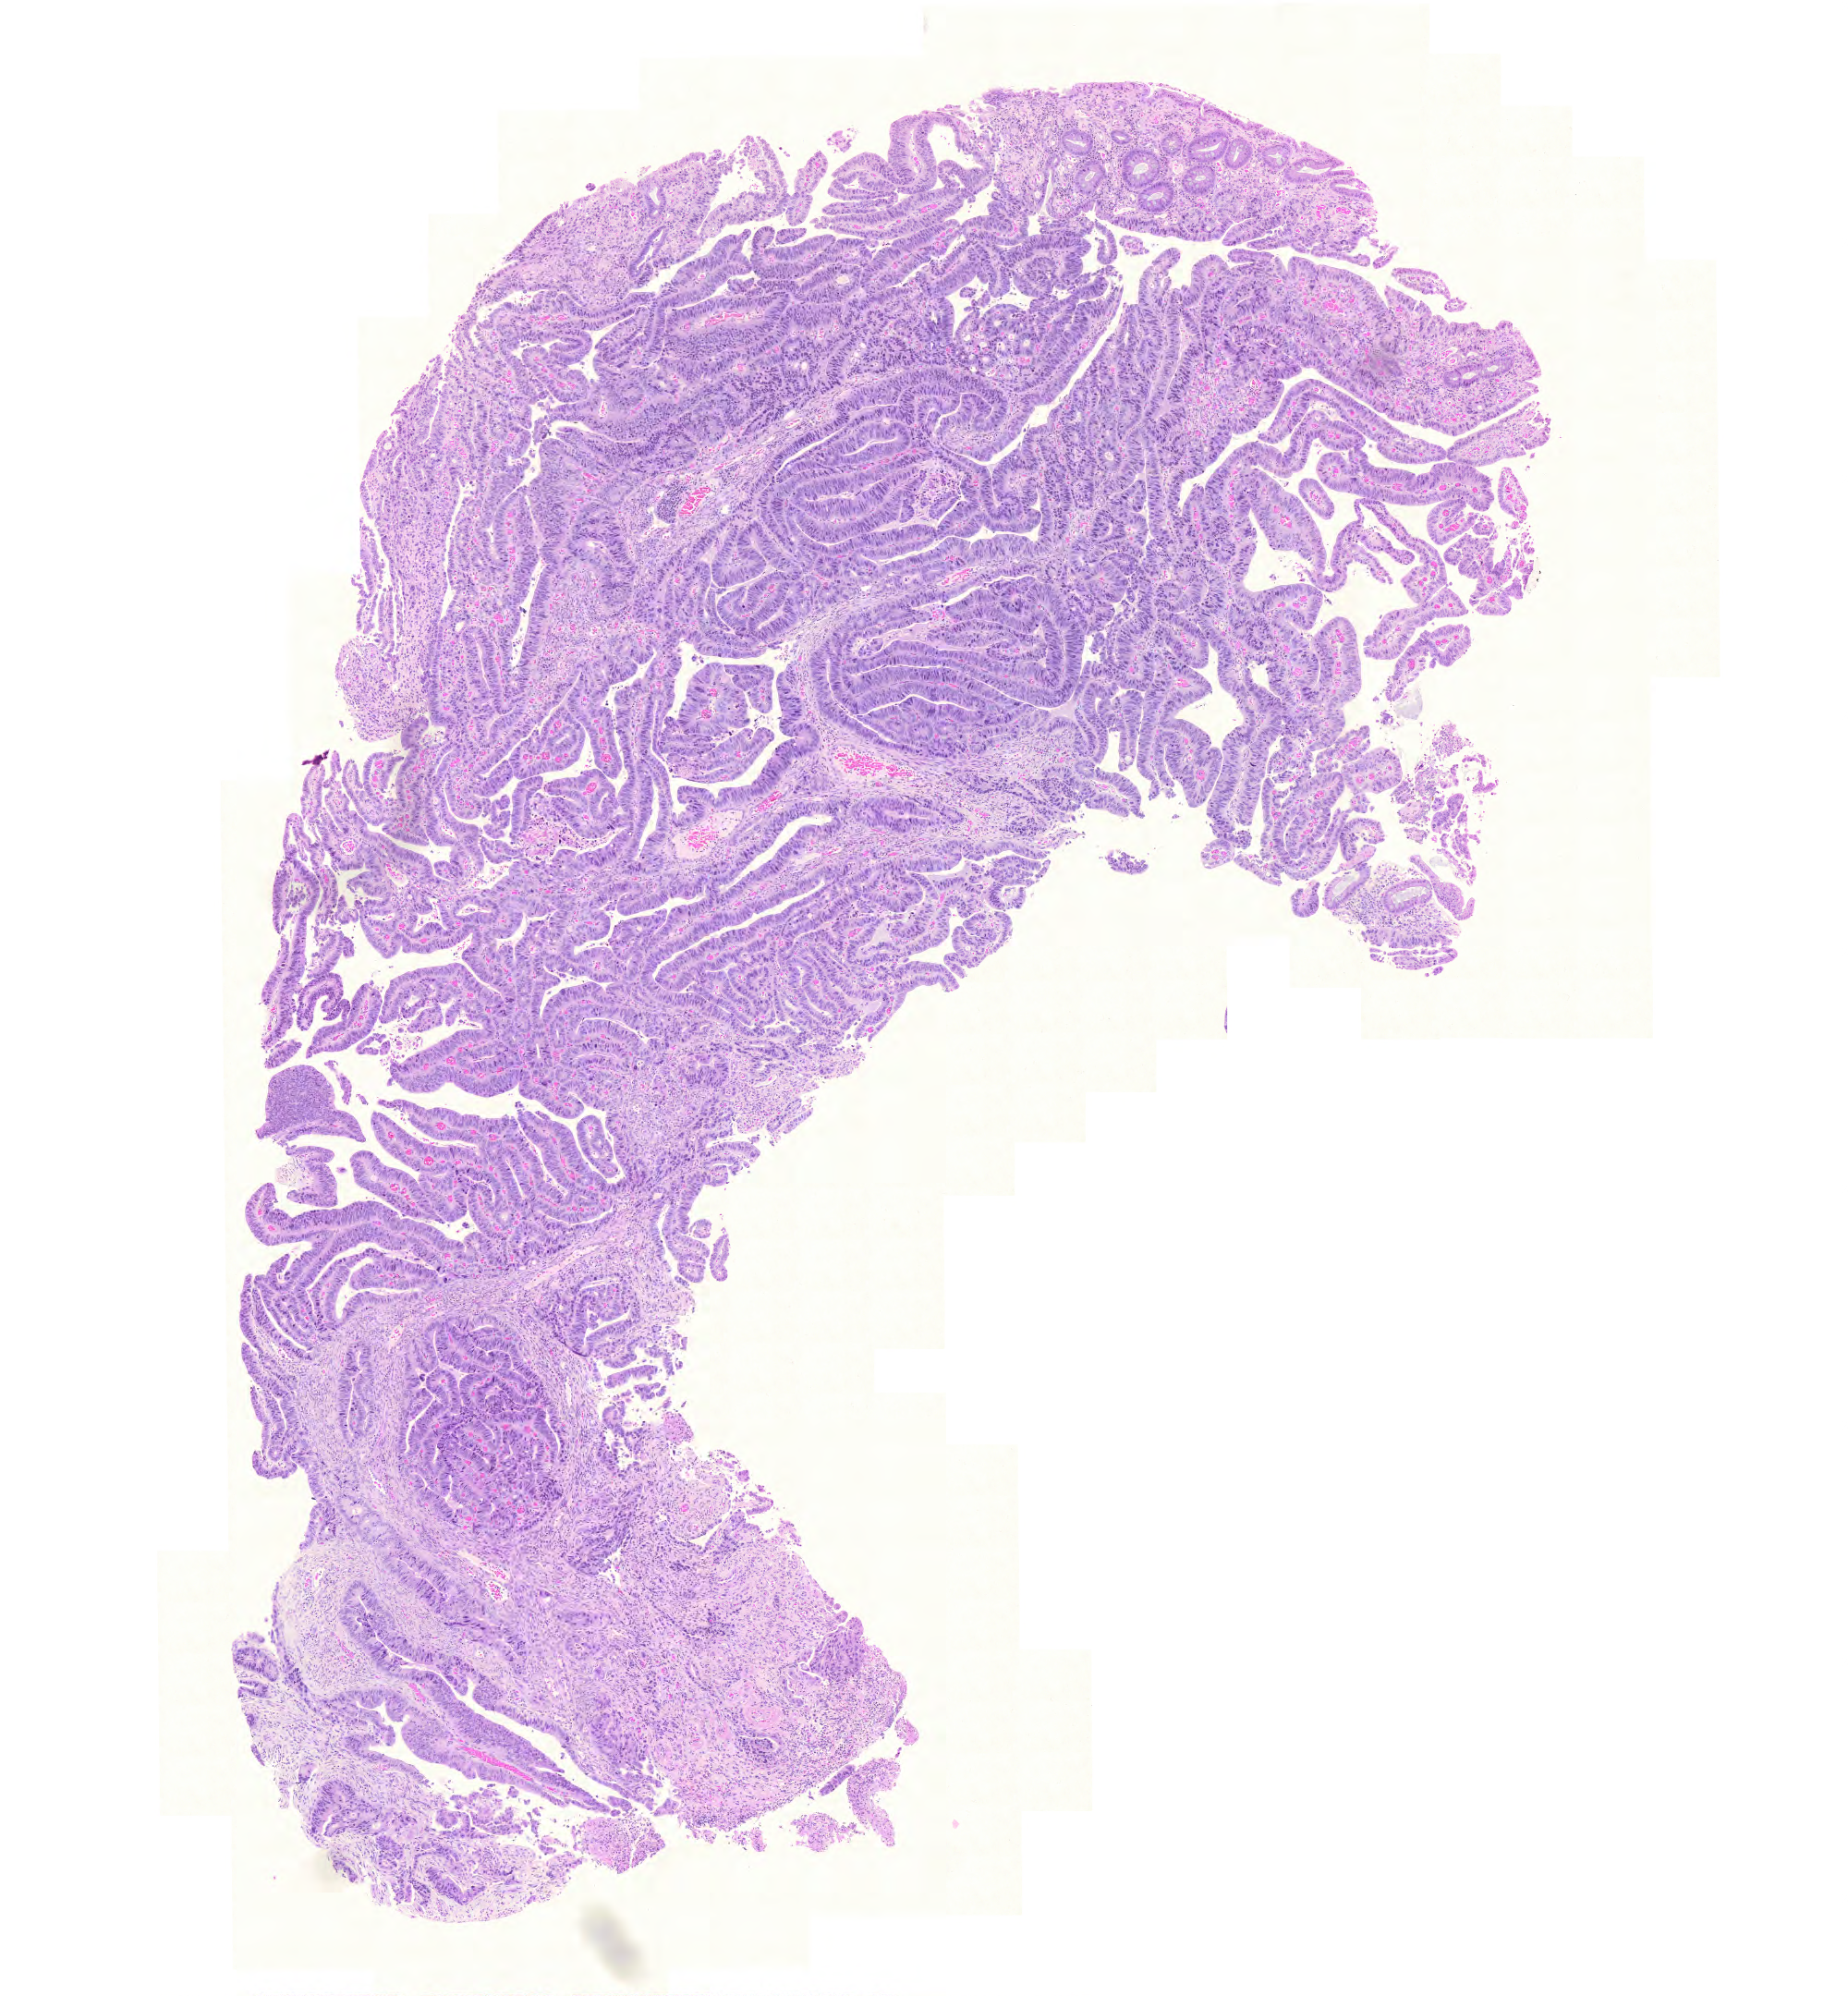
Hematoxylin and eosin (H&E) stained whole-slide image — shown as a low-resolution overview of the whole scanned area (about 7.4 x 8.0 mm, acquisition: 20x scan). Formalin-fixed paraffin-embedded (FFPE) diagnostic section. Colon, primary tumour sample. Patient: male, age at initial diagnosis 72 years.
Histologic diagnosis: Adenocarcinoma, NOS.